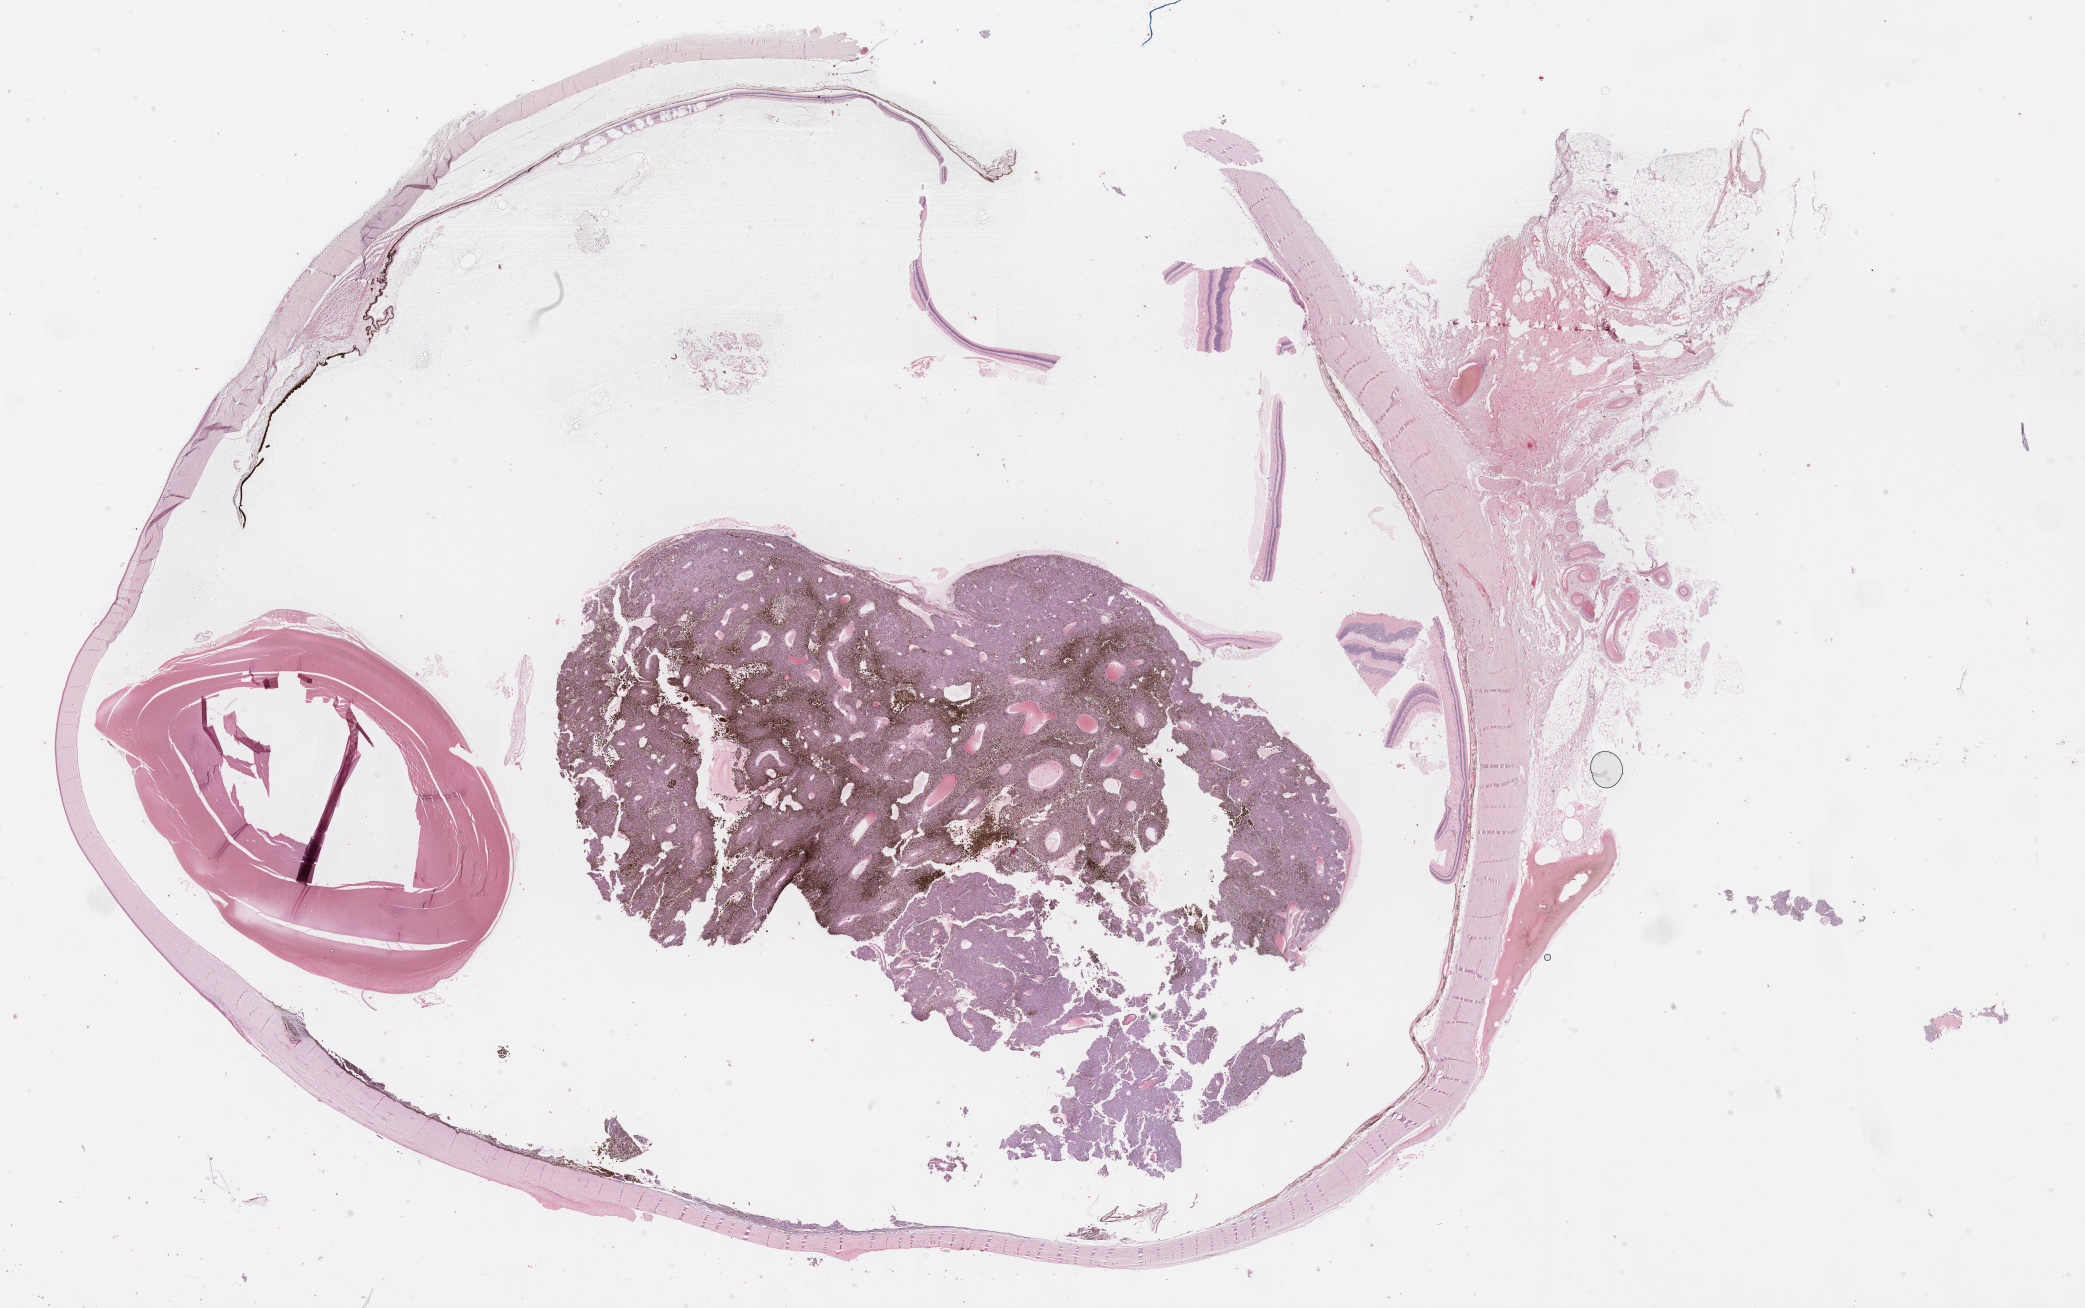
H&E whole-slide image, low-resolution overview of the scanned area, about 33.7 x 21.2 mm (from a 40x scan), formalin-fixed paraffin-embedded (FFPE) diagnostic section, uvea, primary tumour sample. Patient: male, age at initial diagnosis 57 years.
Pathologic diagnosis: Mixed epithelioid and spindle cell melanoma (choroid). Laterality: right. AJCC pathologic stage: IIIB.